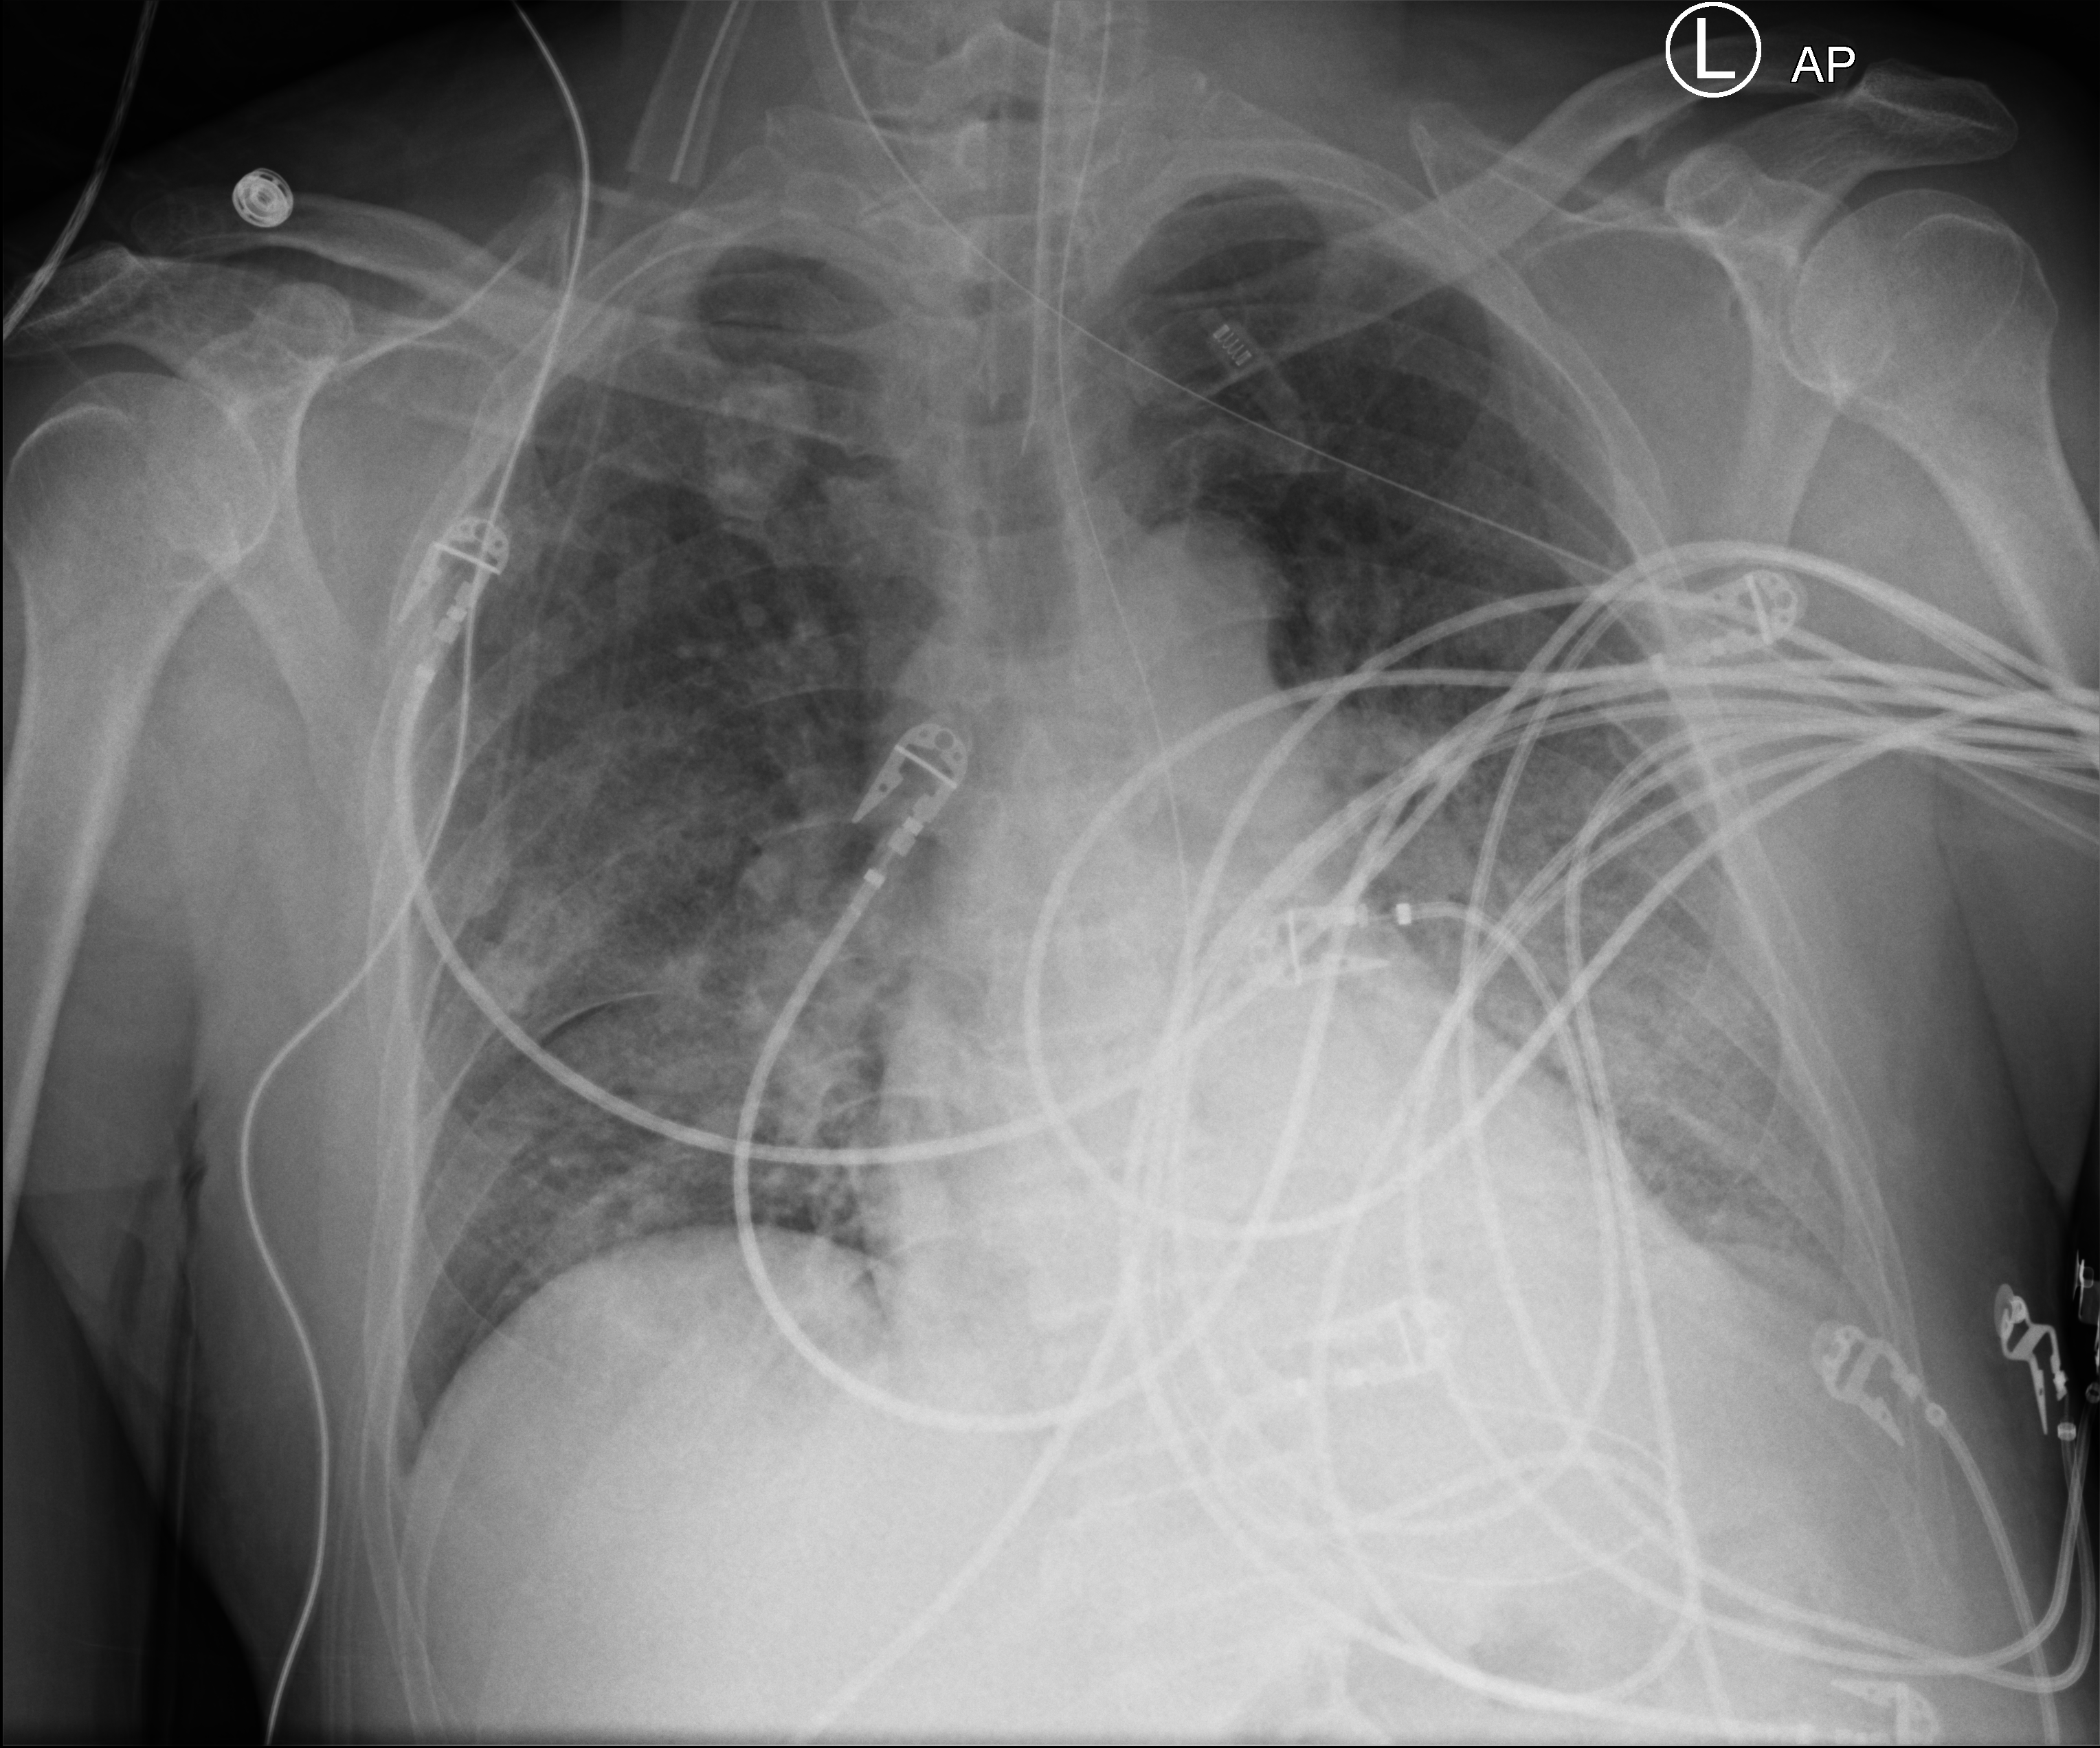
Chest X-ray (portable); anteroposterior (AP) projection. Patient hospitalised with COVID-19; male, aged 60–74 years.
From the hospital-stay record, not from the radiograph (when in the stay this image was taken is not recorded):
- admitted to intensive care during this hospital stay: yes